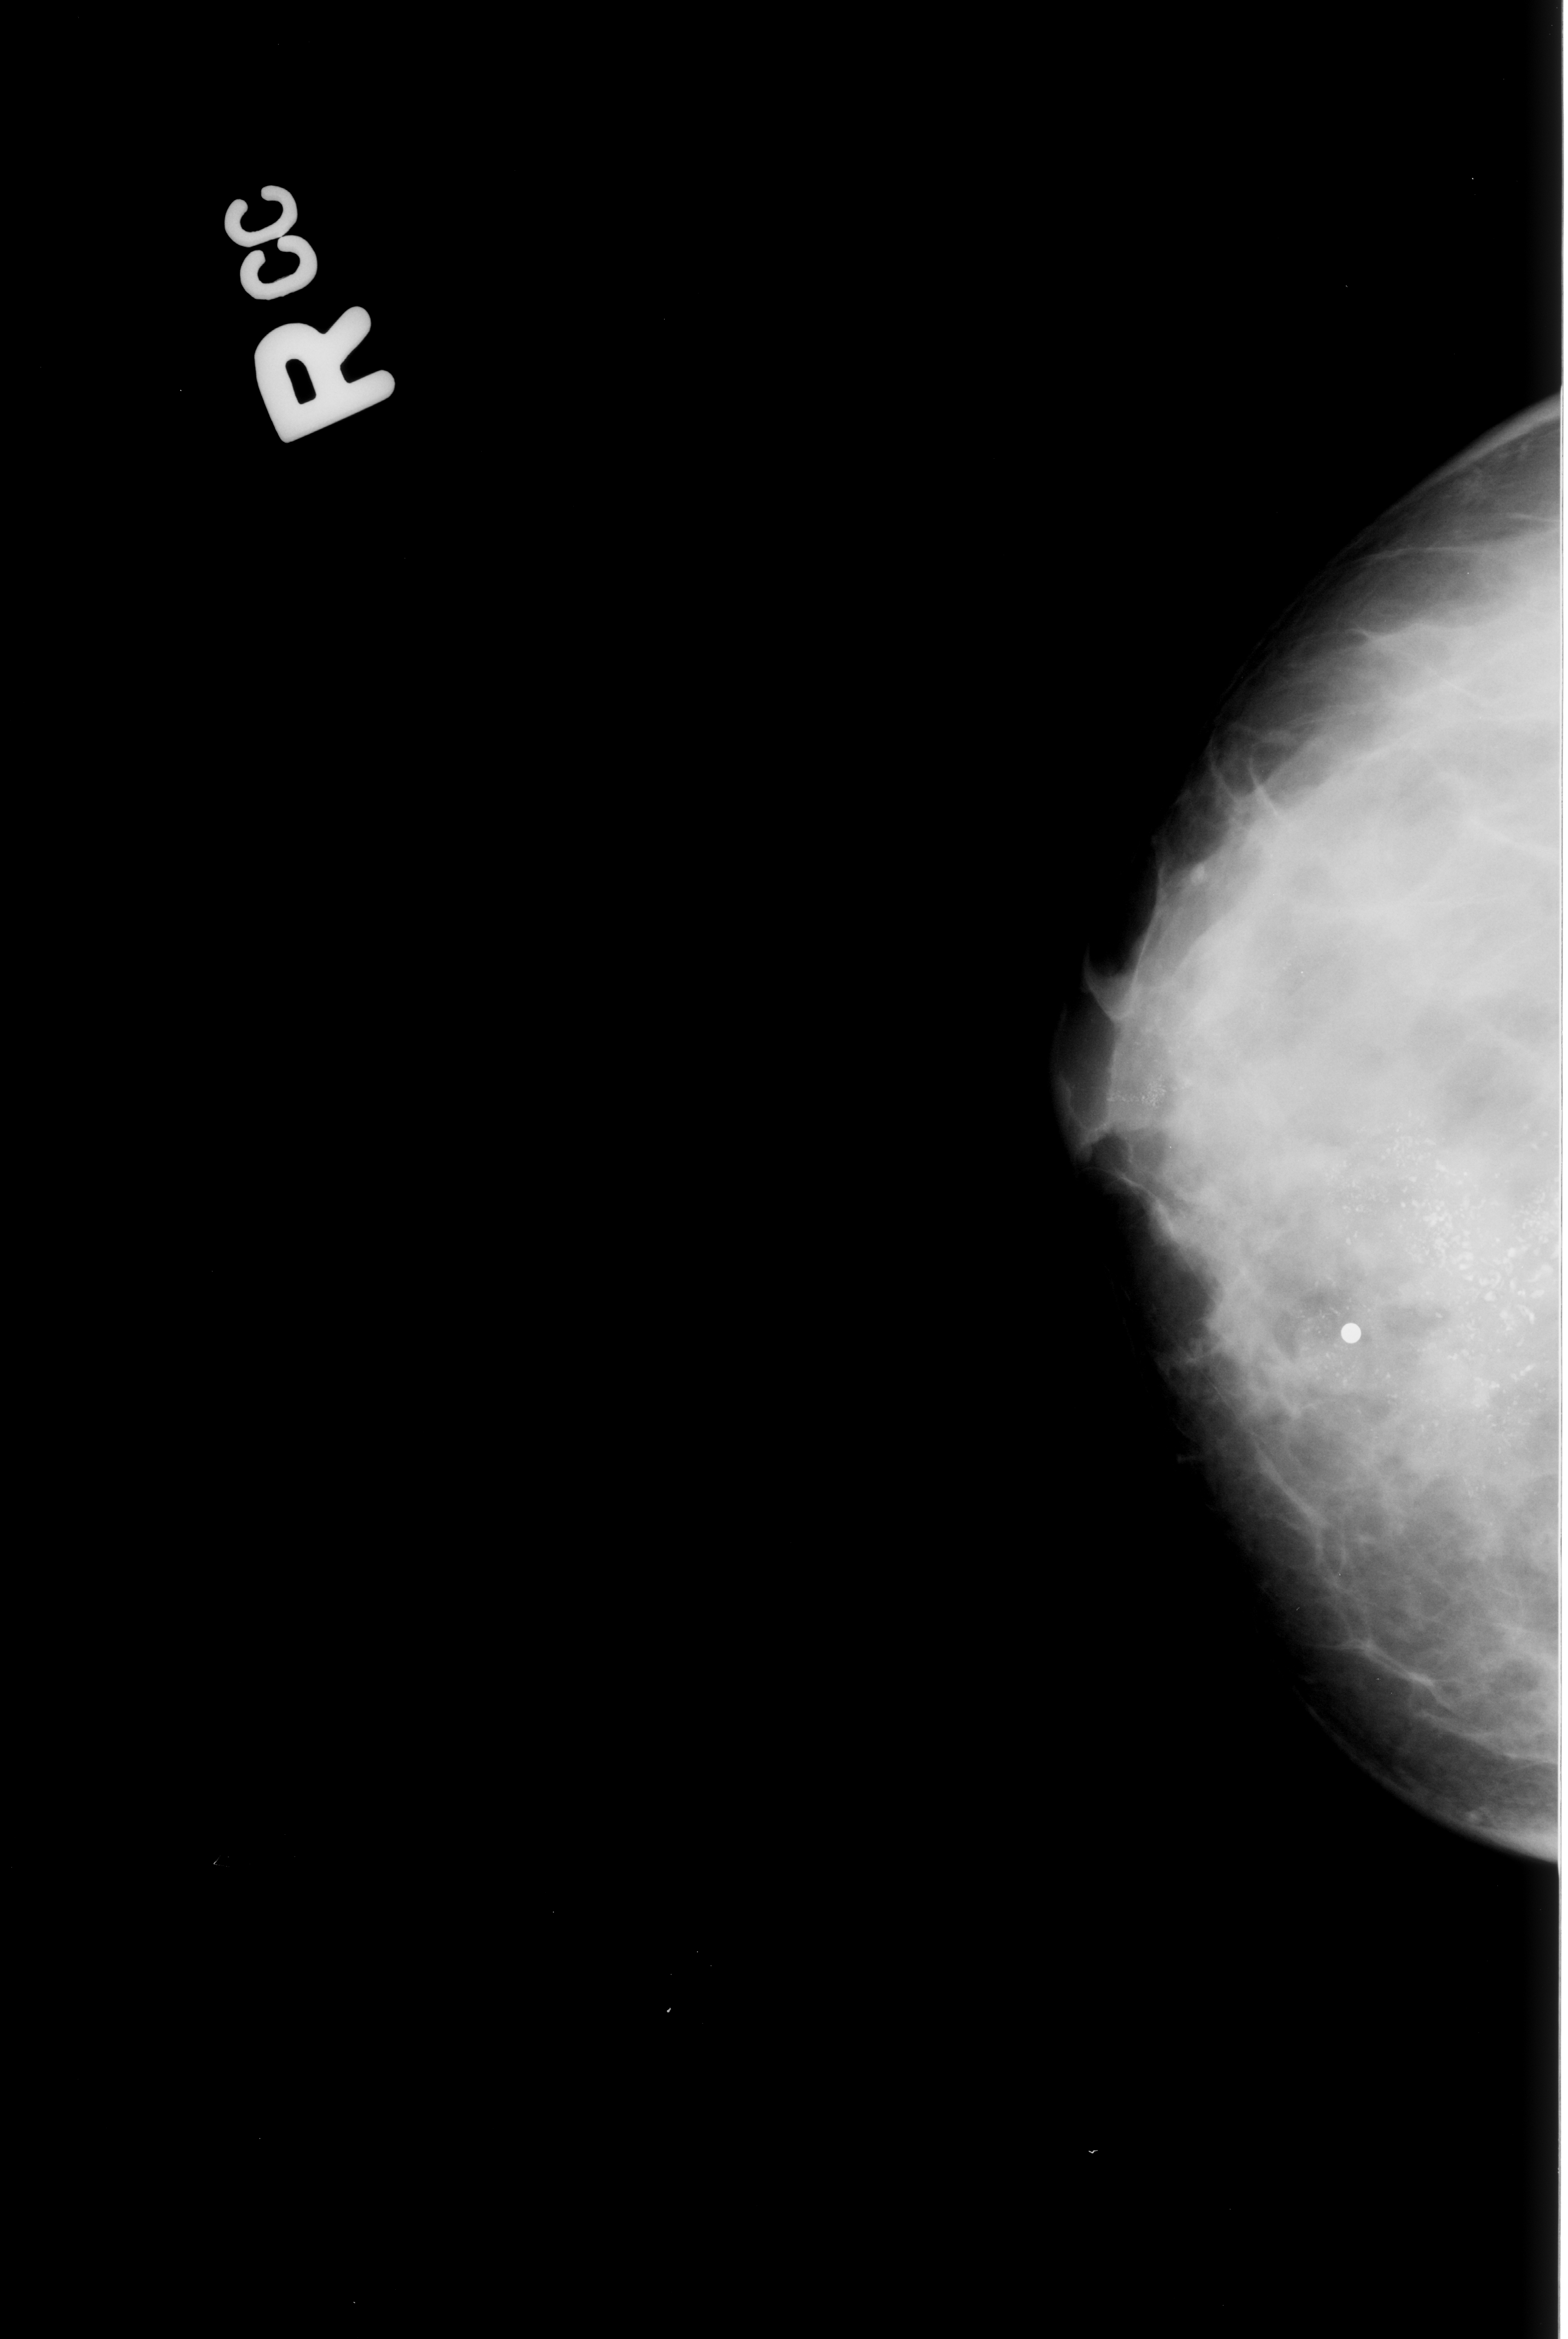
Digitized screen-film mammogram; right breast; craniocaudal (CC) view; BI-RADS breast density category 3 (scale 1–4); 1568 × 2339 image matrix.
Marked abnormalities (boxes around the expert regions of interest):
- calcifications, morphology pleomorphic, distribution regional; BI-RADS assessment category 5; subtlety rating 5 on a 1 (subtle) to 5 (obvious) scale; pathology (as recorded): malignant: bounding box [x1, y1, x2, y2] px = [1059, 924, 1565, 1565]